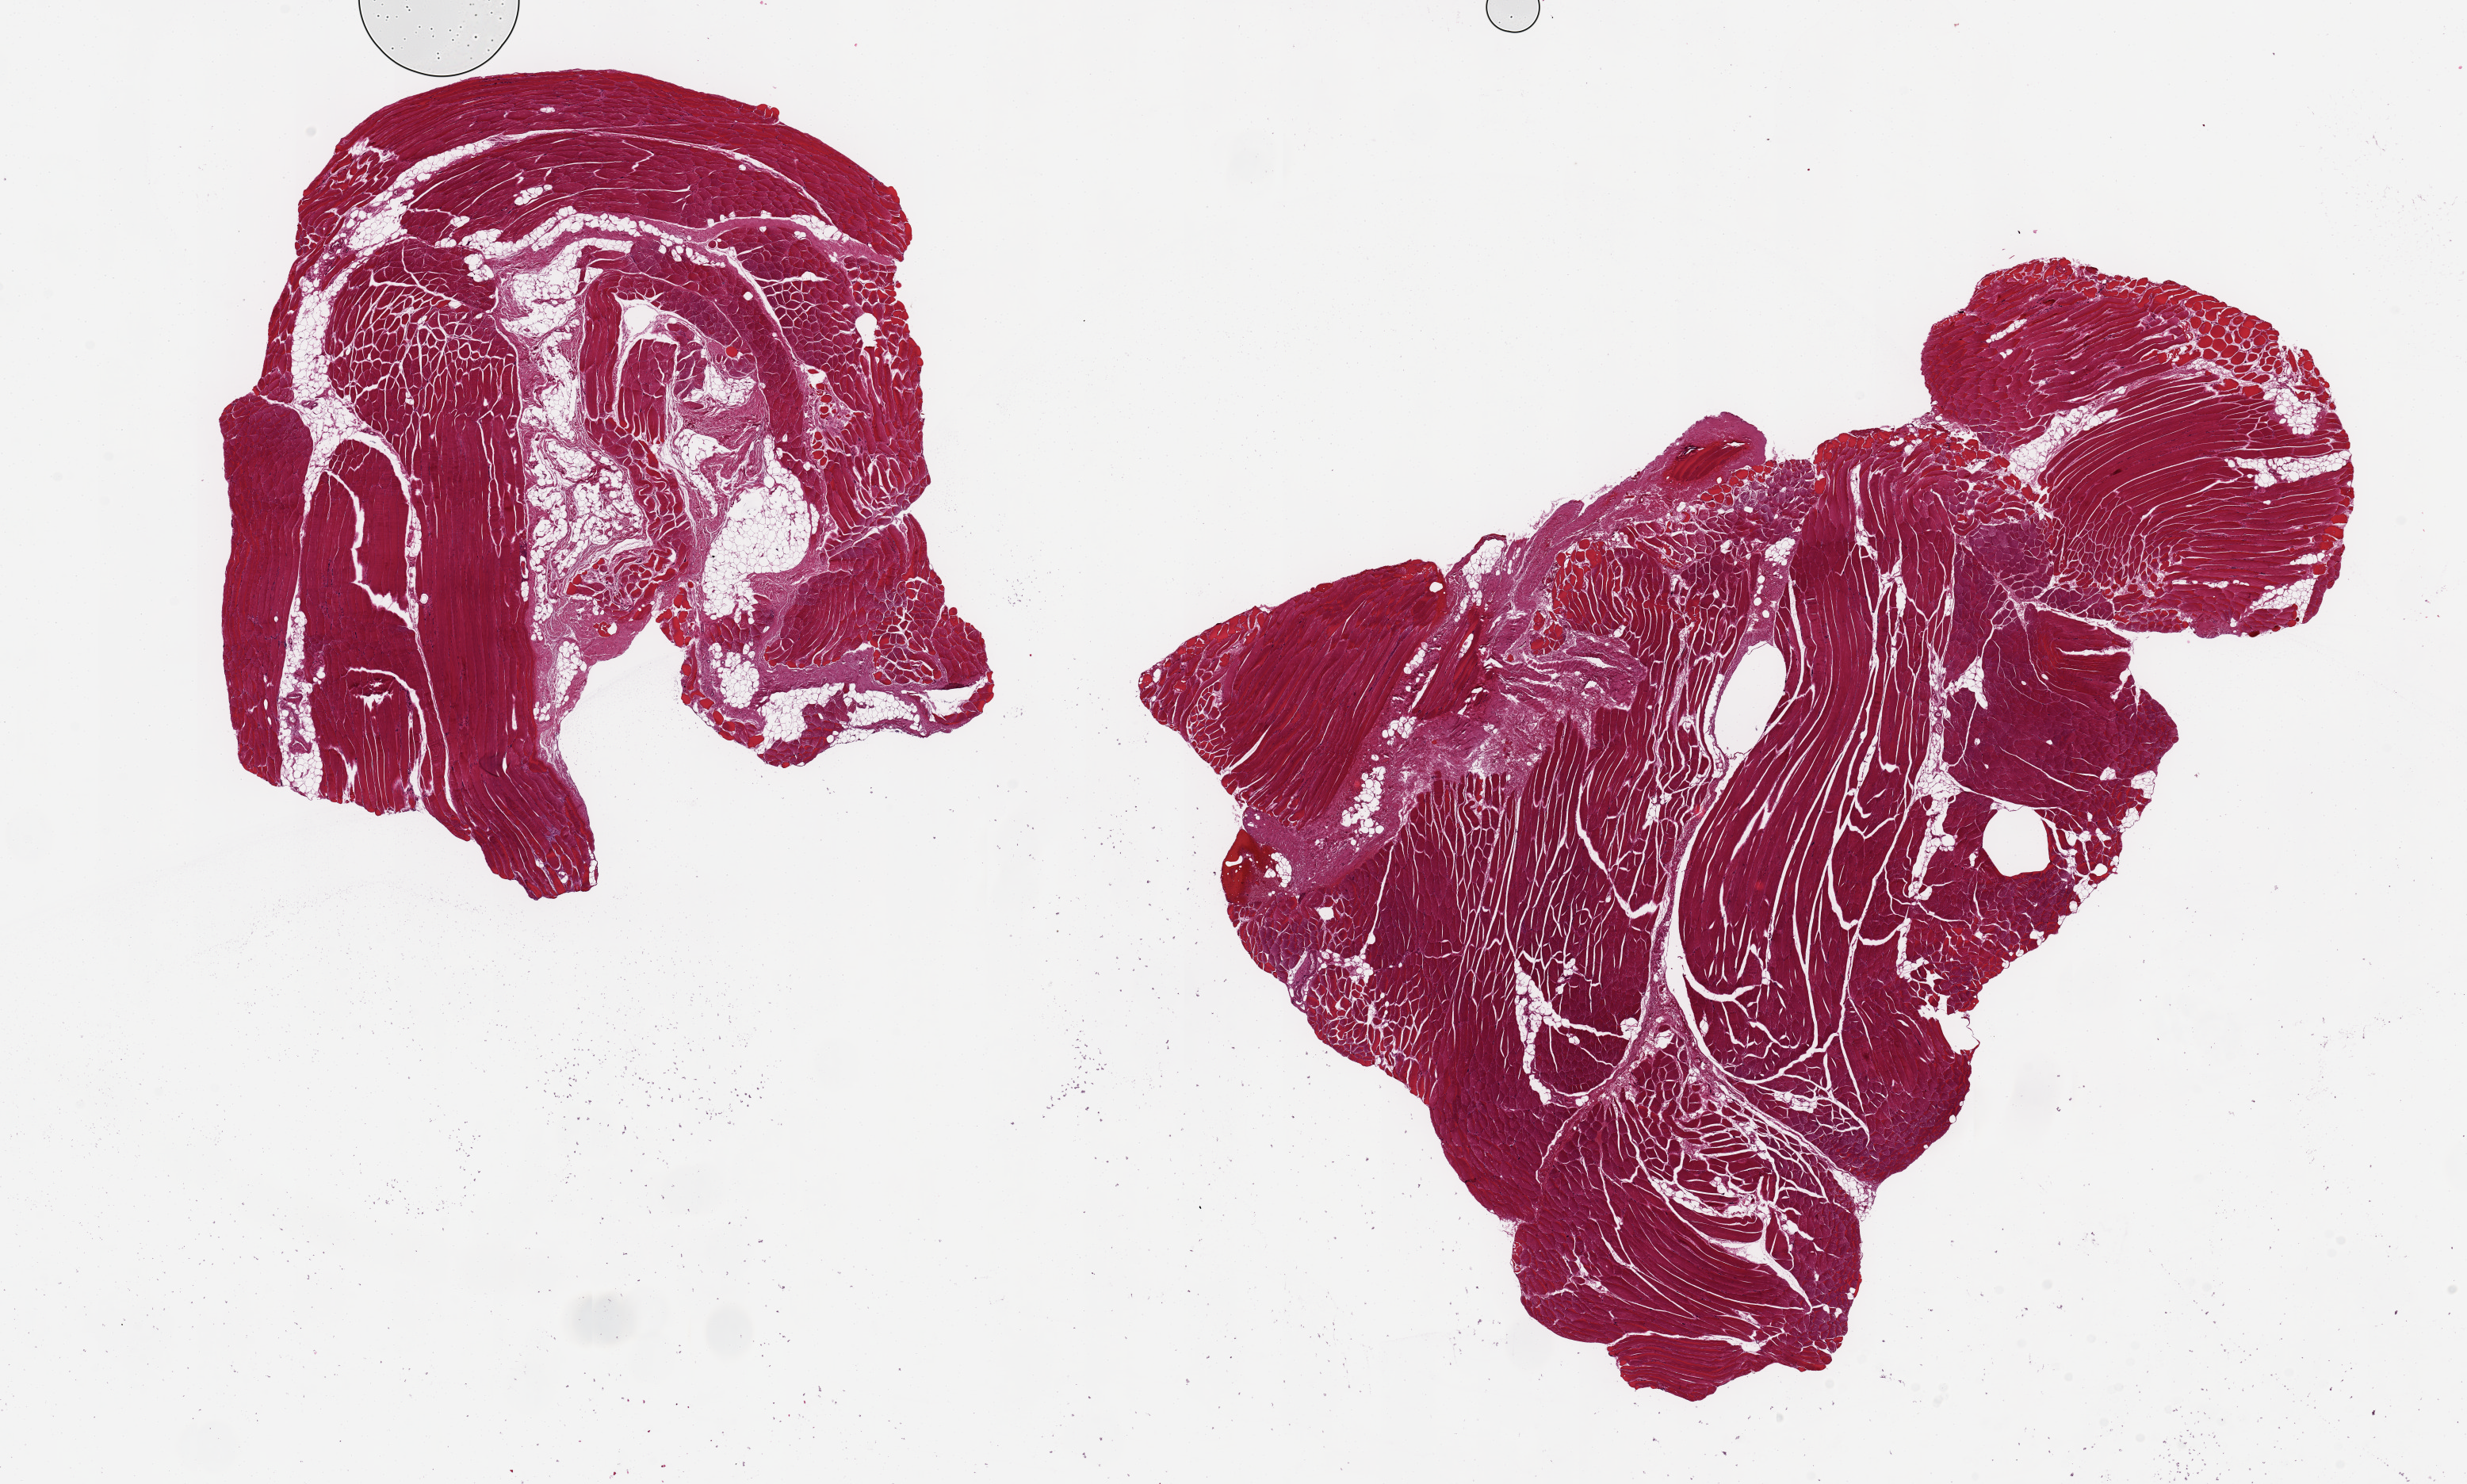
Digitized haematoxylin and eosin-stained section, whole scanned area (about 24.6 x 14.8 mm) shown as a low-resolution overview; PAXgene-fixed, paraffin-embedded tissue; sampled site (target tissue): skeletal muscle; tissue donor sample. Donor: male.
Pathologist's review note for this sample: 2 pieces 10x9 & 8x5 mm; ~20% interspersed adipose in smaller aliquot, <5% in larger; no obvious atrophy.